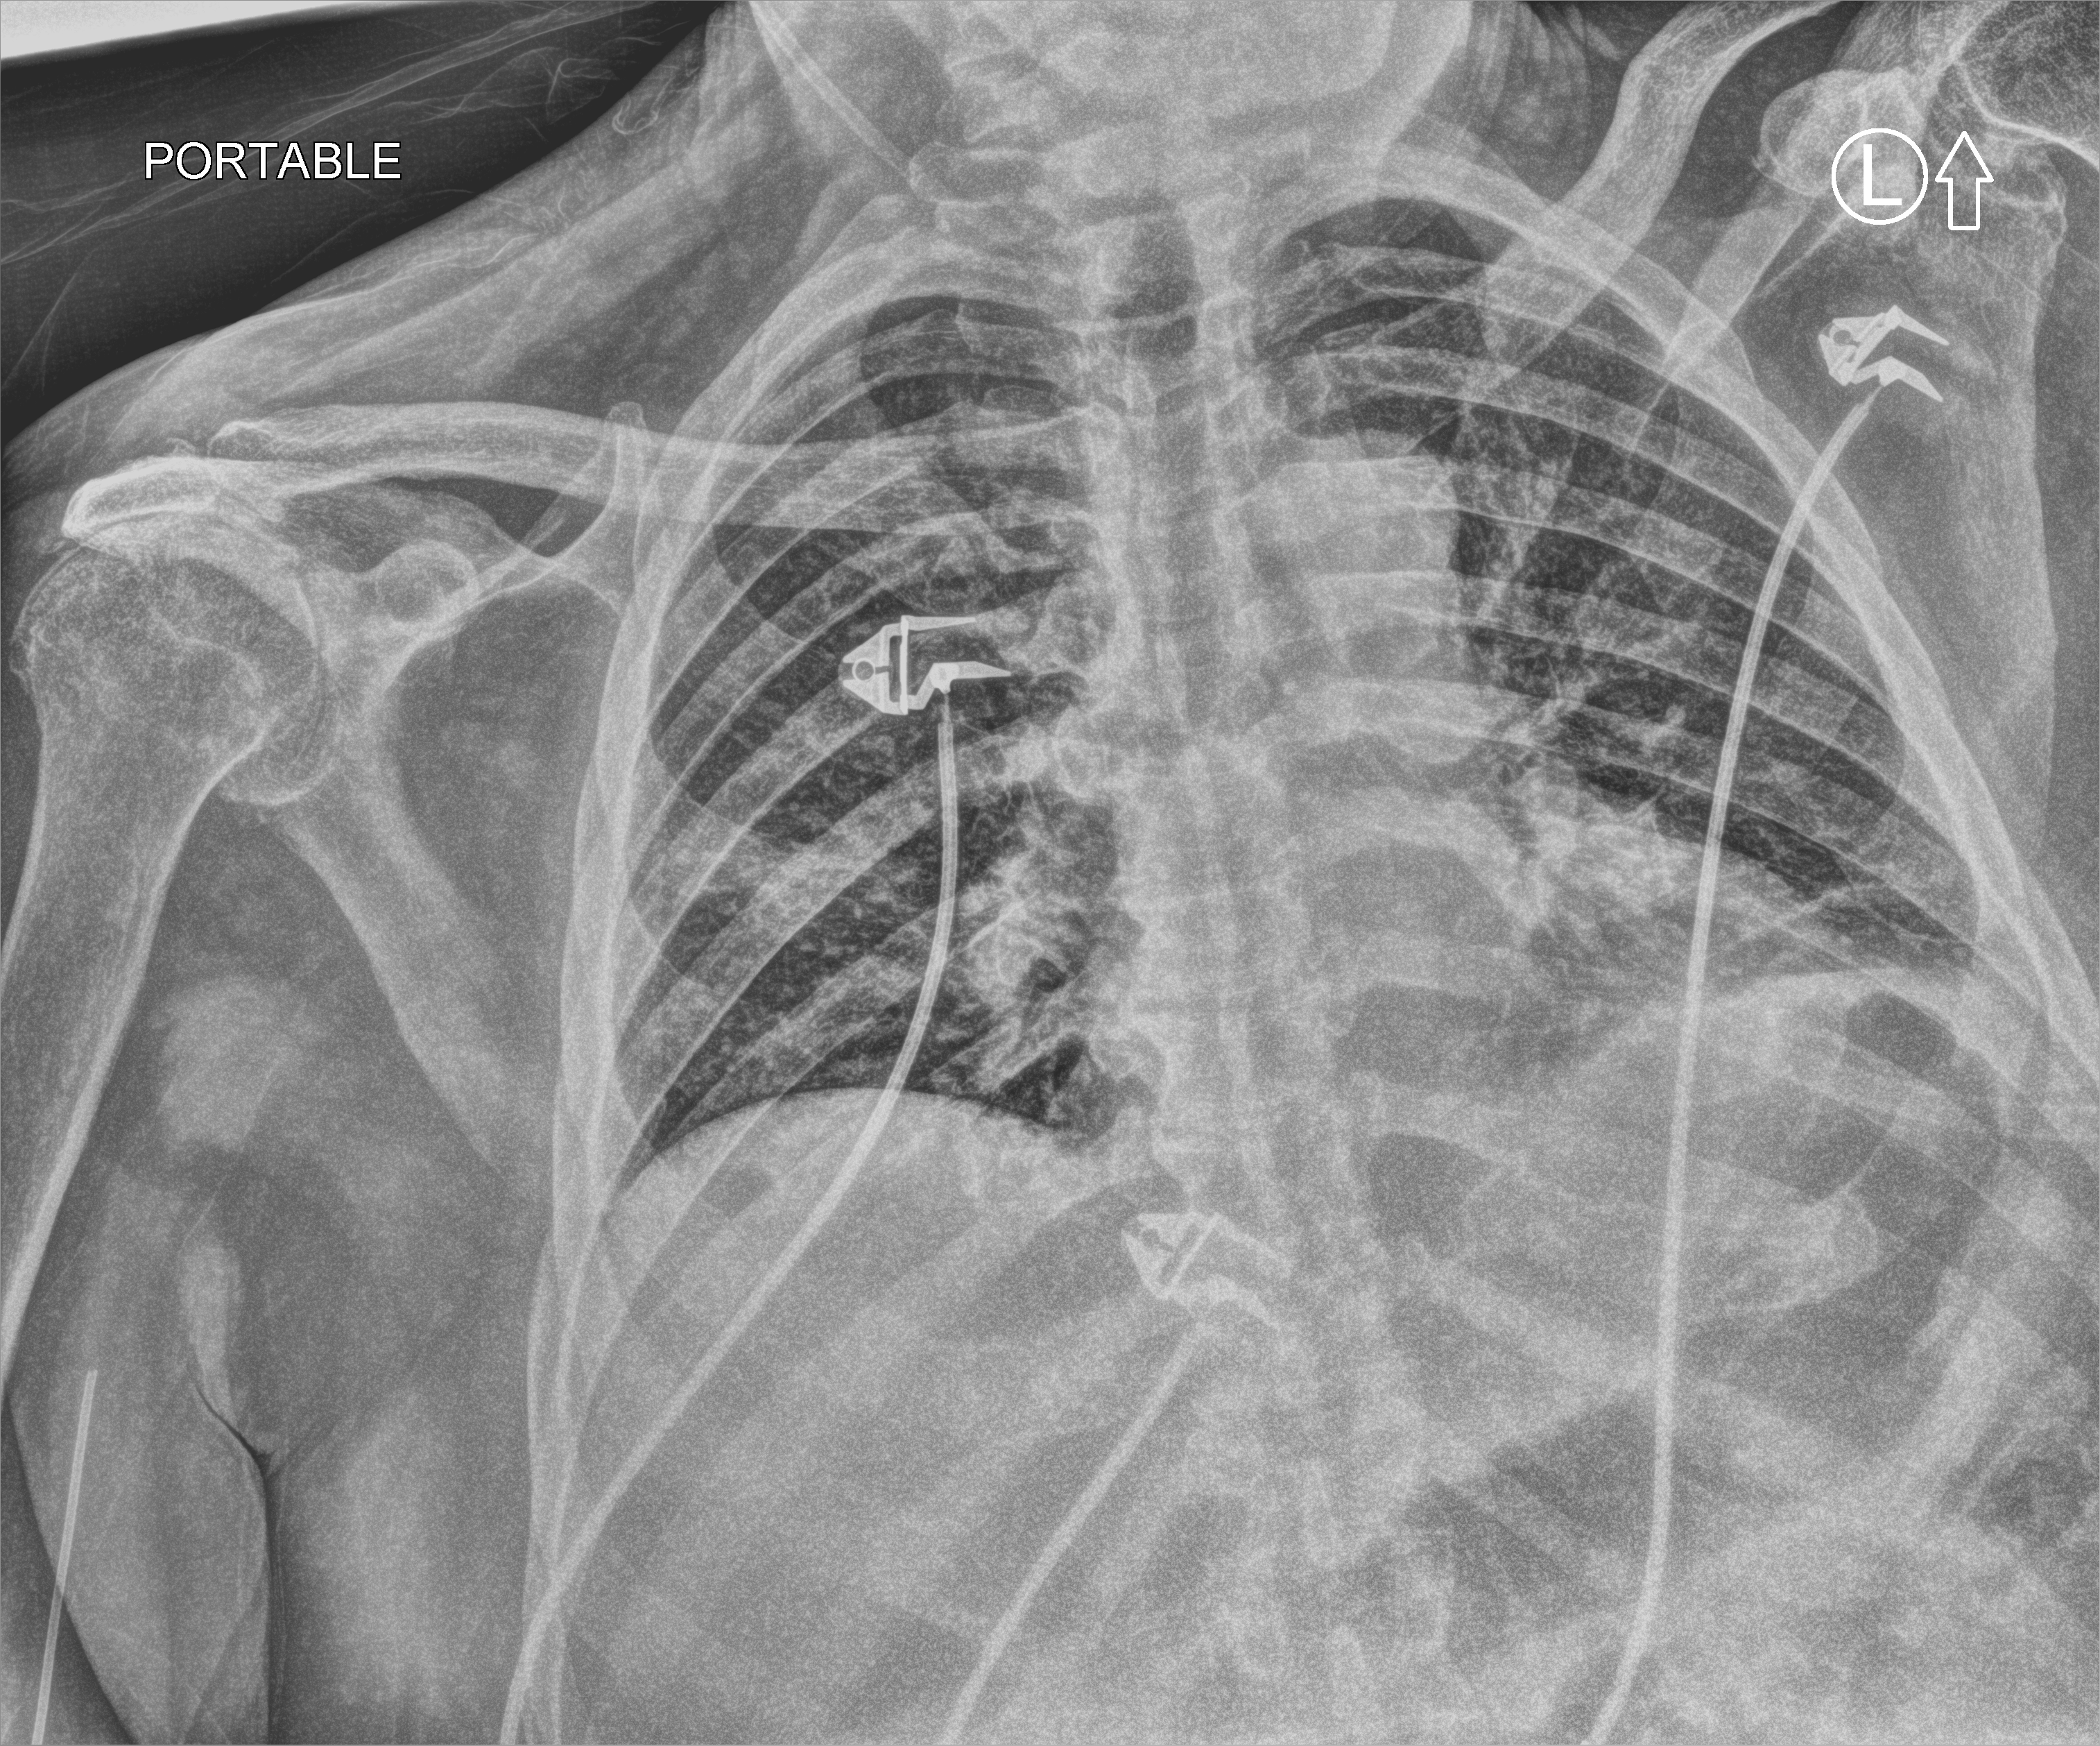
Bedside chest radiograph (computed radiography), anteroposterior (AP) projection. Patient hospitalised with COVID-19; male, aged 75–90 years.
Admission-level facts for this patient (not findings on this image; timing relative to this image not recorded): mechanically ventilated during this hospital stay: yes; admitted to intensive care during this hospital stay: yes.